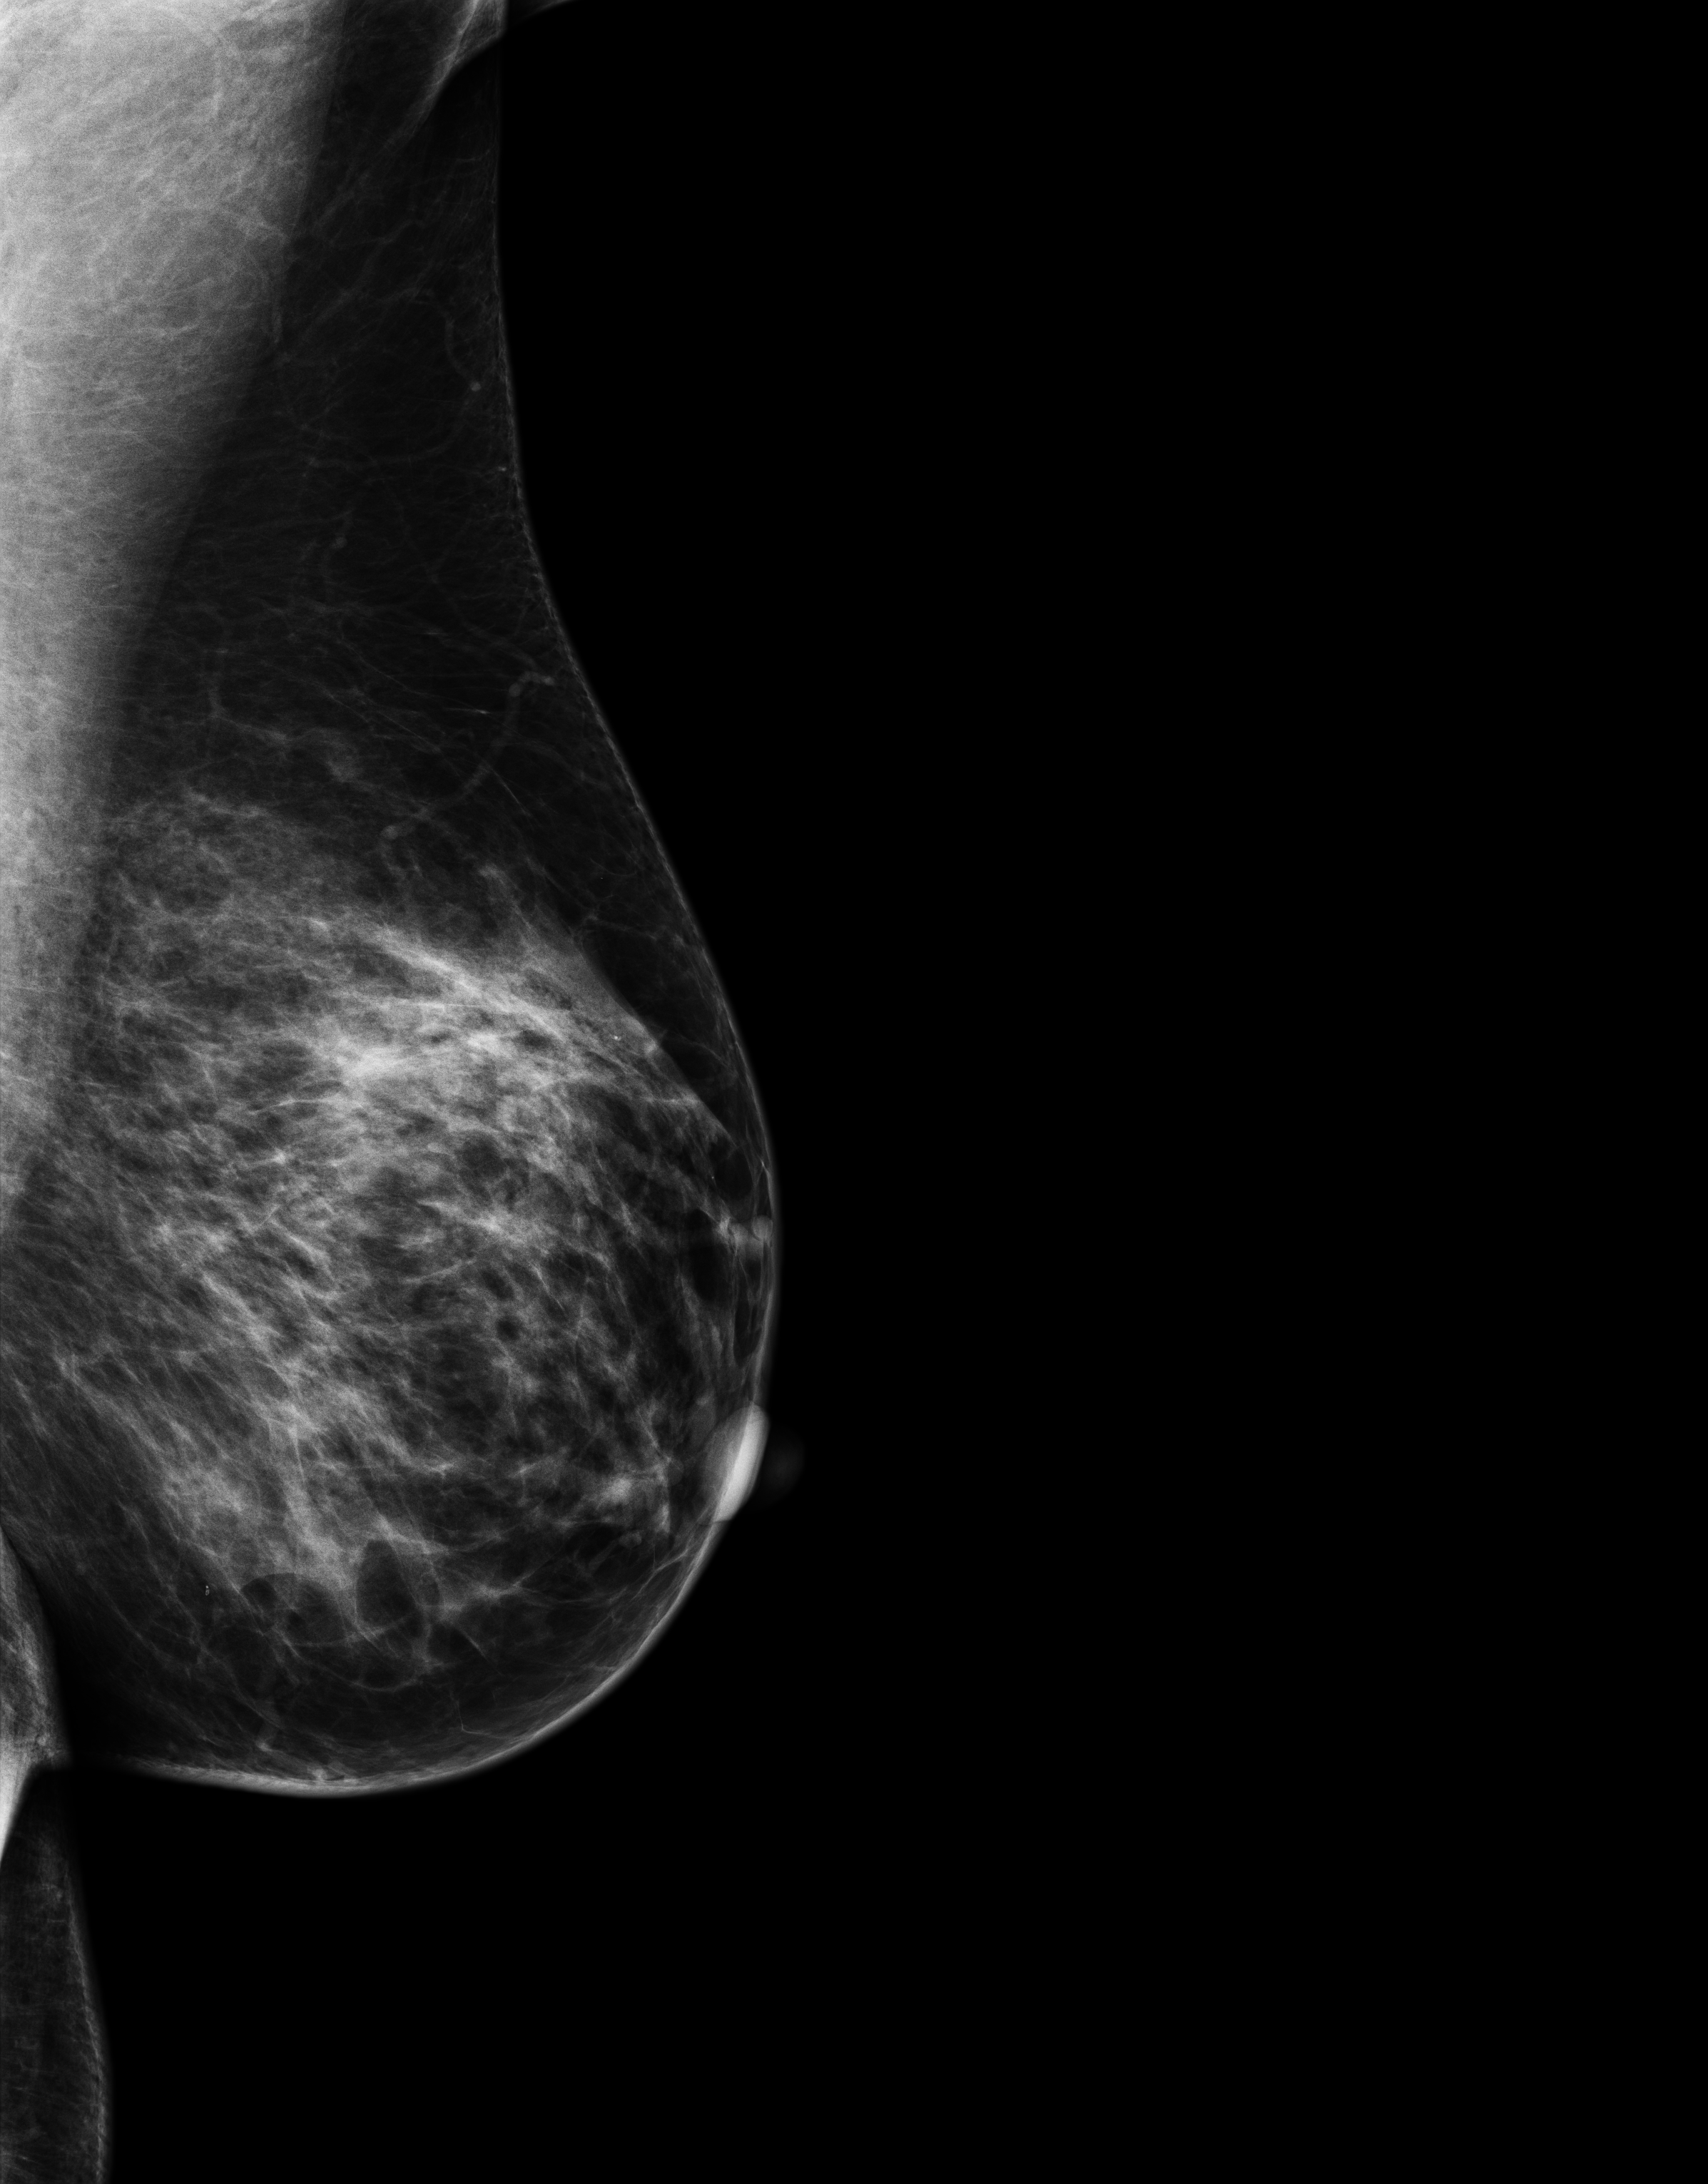
Screening examination; compressed breast thickness 70 mm. Patient: female, 50 years.
Image type: full-field digital mammogram. Breast: left. Projection: medio-lateral oblique projection.